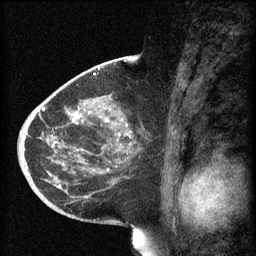
Breast MRI (dynamic contrast-enhanced), one sagittal slice; 3 images stored at this slice position (order not interpretable as contrast timing); 1.5 T; TE 4.2 ms, TR 8.1 ms; 2 mm slice thickness; 256 × 256 image matrix. Patient: female, 44 years.
Structures marked on this image (semi-automatic segmentation, software-assisted and operator-edited):
- analysis volume of interest (the breast-tissue region the enhancement analysis was run in; not a lesion): bounding box <59,110,146,169> (left, top, right, bottom; pixels)
- tumour enhancement mask (voxels above the 70 % enhancement threshold inside the analysis volume of interest): <72,114,127,127>